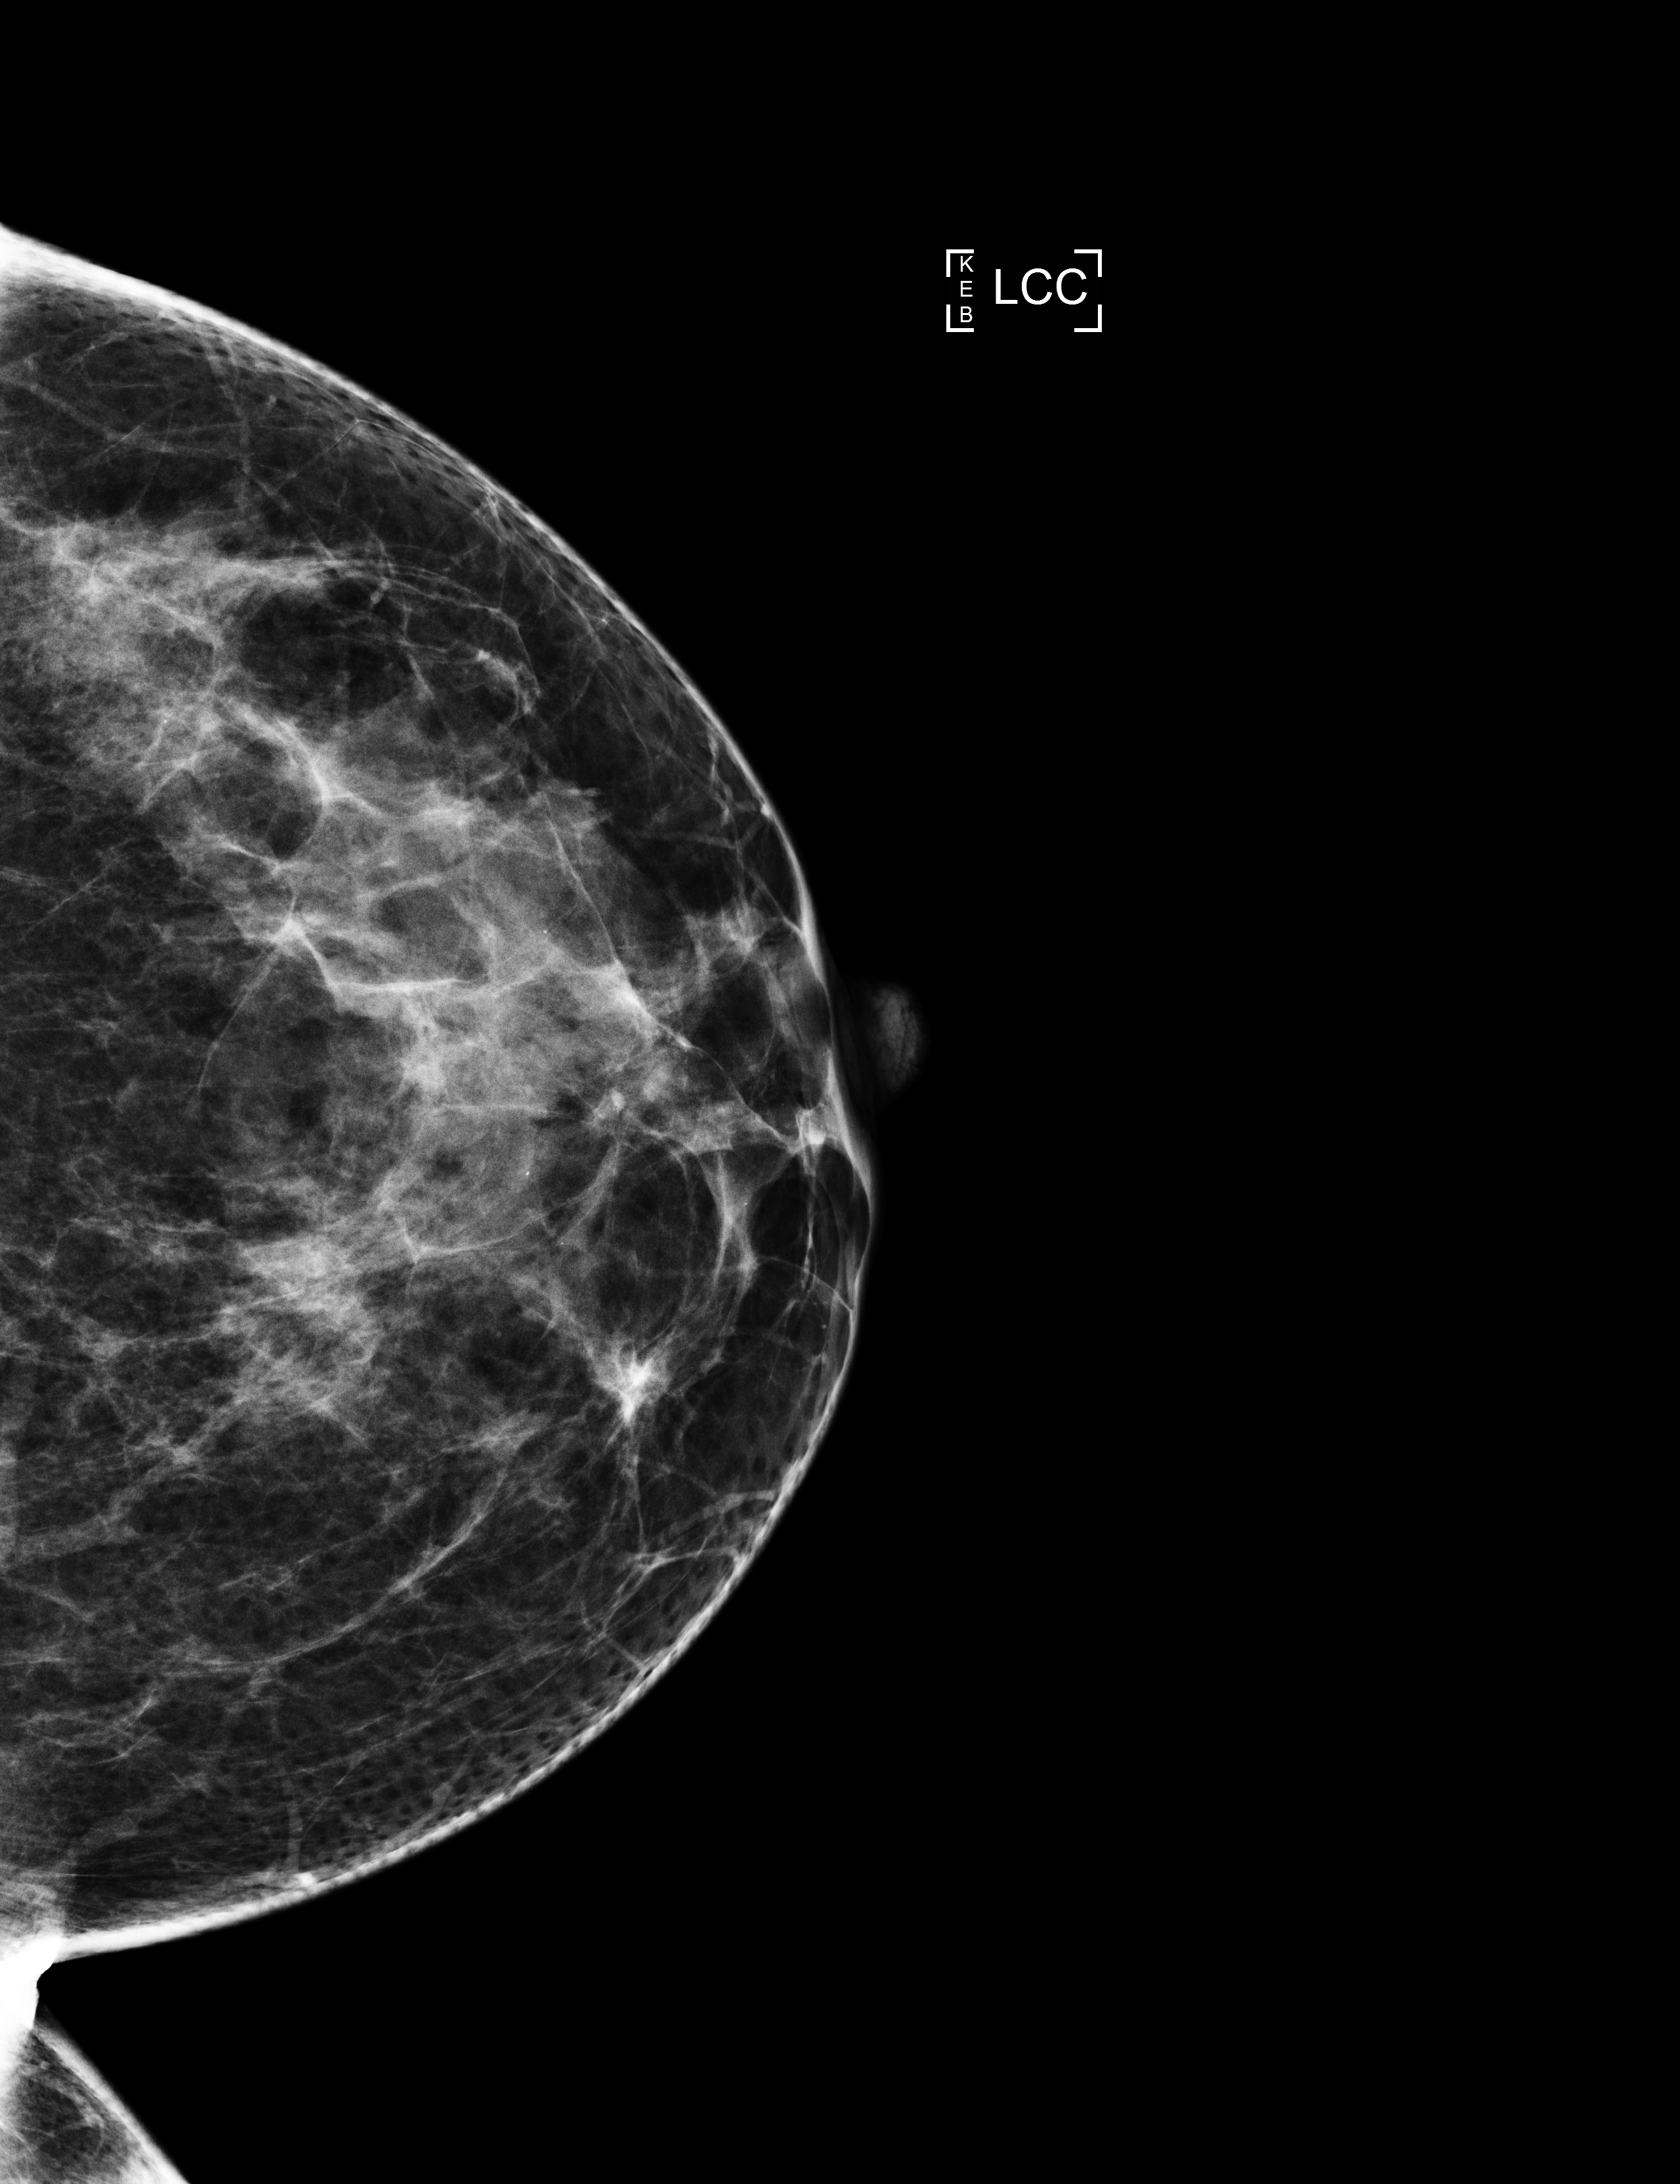
Screening examination; compressed breast thickness 59 mm; system: Selenia Dimensions. Patient: female, 41 years.
Image type: full-field digital mammogram. Breast: left. Projection: cranio-caudal projection.